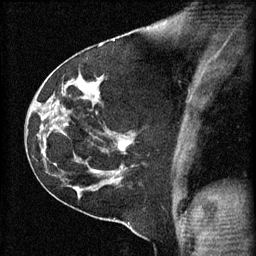
Breast MRI (dynamic contrast-enhanced), one sagittal slice. 3 images stored at this slice position (order not interpretable as contrast timing). 1.5 T. TE 4.2 ms, TR 11 ms. 256 × 256 image matrix. Female patient, age 45 years.
Structures marked on this image (semi-automatic segmentation, software-assisted and operator-edited):
- analysis volume of interest (the breast-tissue region the enhancement analysis was run in; not a lesion): box from (x=104, y=130) to (x=137, y=171) px
- tumour enhancement mask (voxels above the 70 % enhancement threshold inside the analysis volume of interest): (x=120, y=142)–(x=127, y=151)